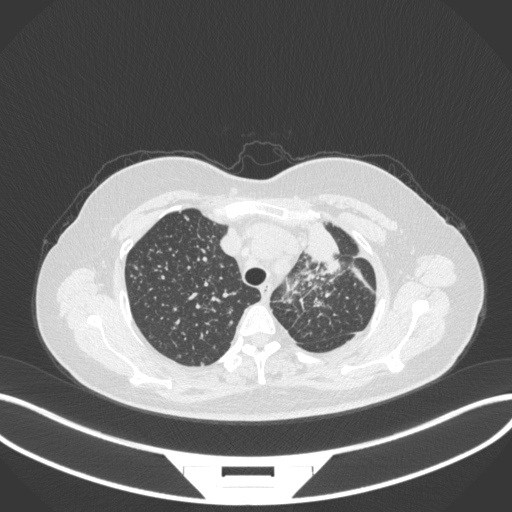
Chest CT, one axial slice. Position 265 of 348 along the scan axis. Lung window (W 1500 / L -600 HU). 1 mm slice thickness. 512 × 512 image matrix. Patient: female, 49 years. From the clinical record (not read from this slice): clinical TNM (as recorded): T1c N0 M1.
Annotated regions visible in this slice (rectangle marked by the reading radiologist):
- lung tumour (recorded histology: adenocarcinoma): bounding box <298,213,342,269> (left, top, right, bottom; pixels)